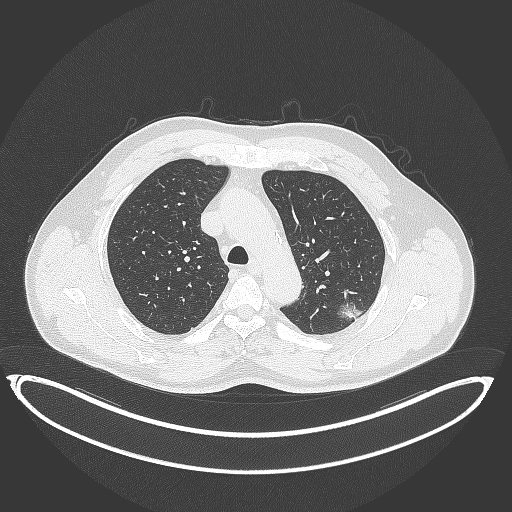
Chest CT, one axial slice. Slice 267 of 399 in the series (ordered by position). Reconstruction kernel B70f. Lung window (W 1500 / L -600 HU). 1 mm slice thickness. 512 × 512 image matrix, field of view 469 × 469 mm. Male patient, age 58 years. Case-level facts recorded for this patient, not image findings: clinical TNM (as recorded): T1c N0 M0.
Annotated regions visible in this slice (bounding box drawn by a radiologist):
- lung tumour (recorded histology: adenocarcinoma): bounding box <337,296,367,326> (left, top, right, bottom; pixels)